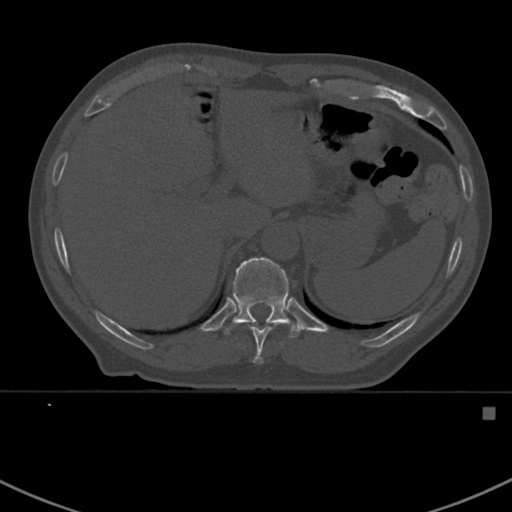
CT including the spine, one axial slice; slice 356 of 412 in the series (ordered by position); reconstruction kernel Br40s; 120 kVp; bone window (W 1800 / L 400 HU); 1.5 mm slice thickness; 512 × 512 image matrix, field of view 358 × 358 mm. Male patient, age 59 years. From the clinical record (not read from this slice): primary cancer: prostate.
Structures marked on this image (semi-automatic segmentation, software-assisted and operator-edited):
- T10 vertebra: bounding box (x1, y1, x2, y2) in pixels: (237, 322, 284, 364)
- T11 vertebra: (207, 257, 303, 338)